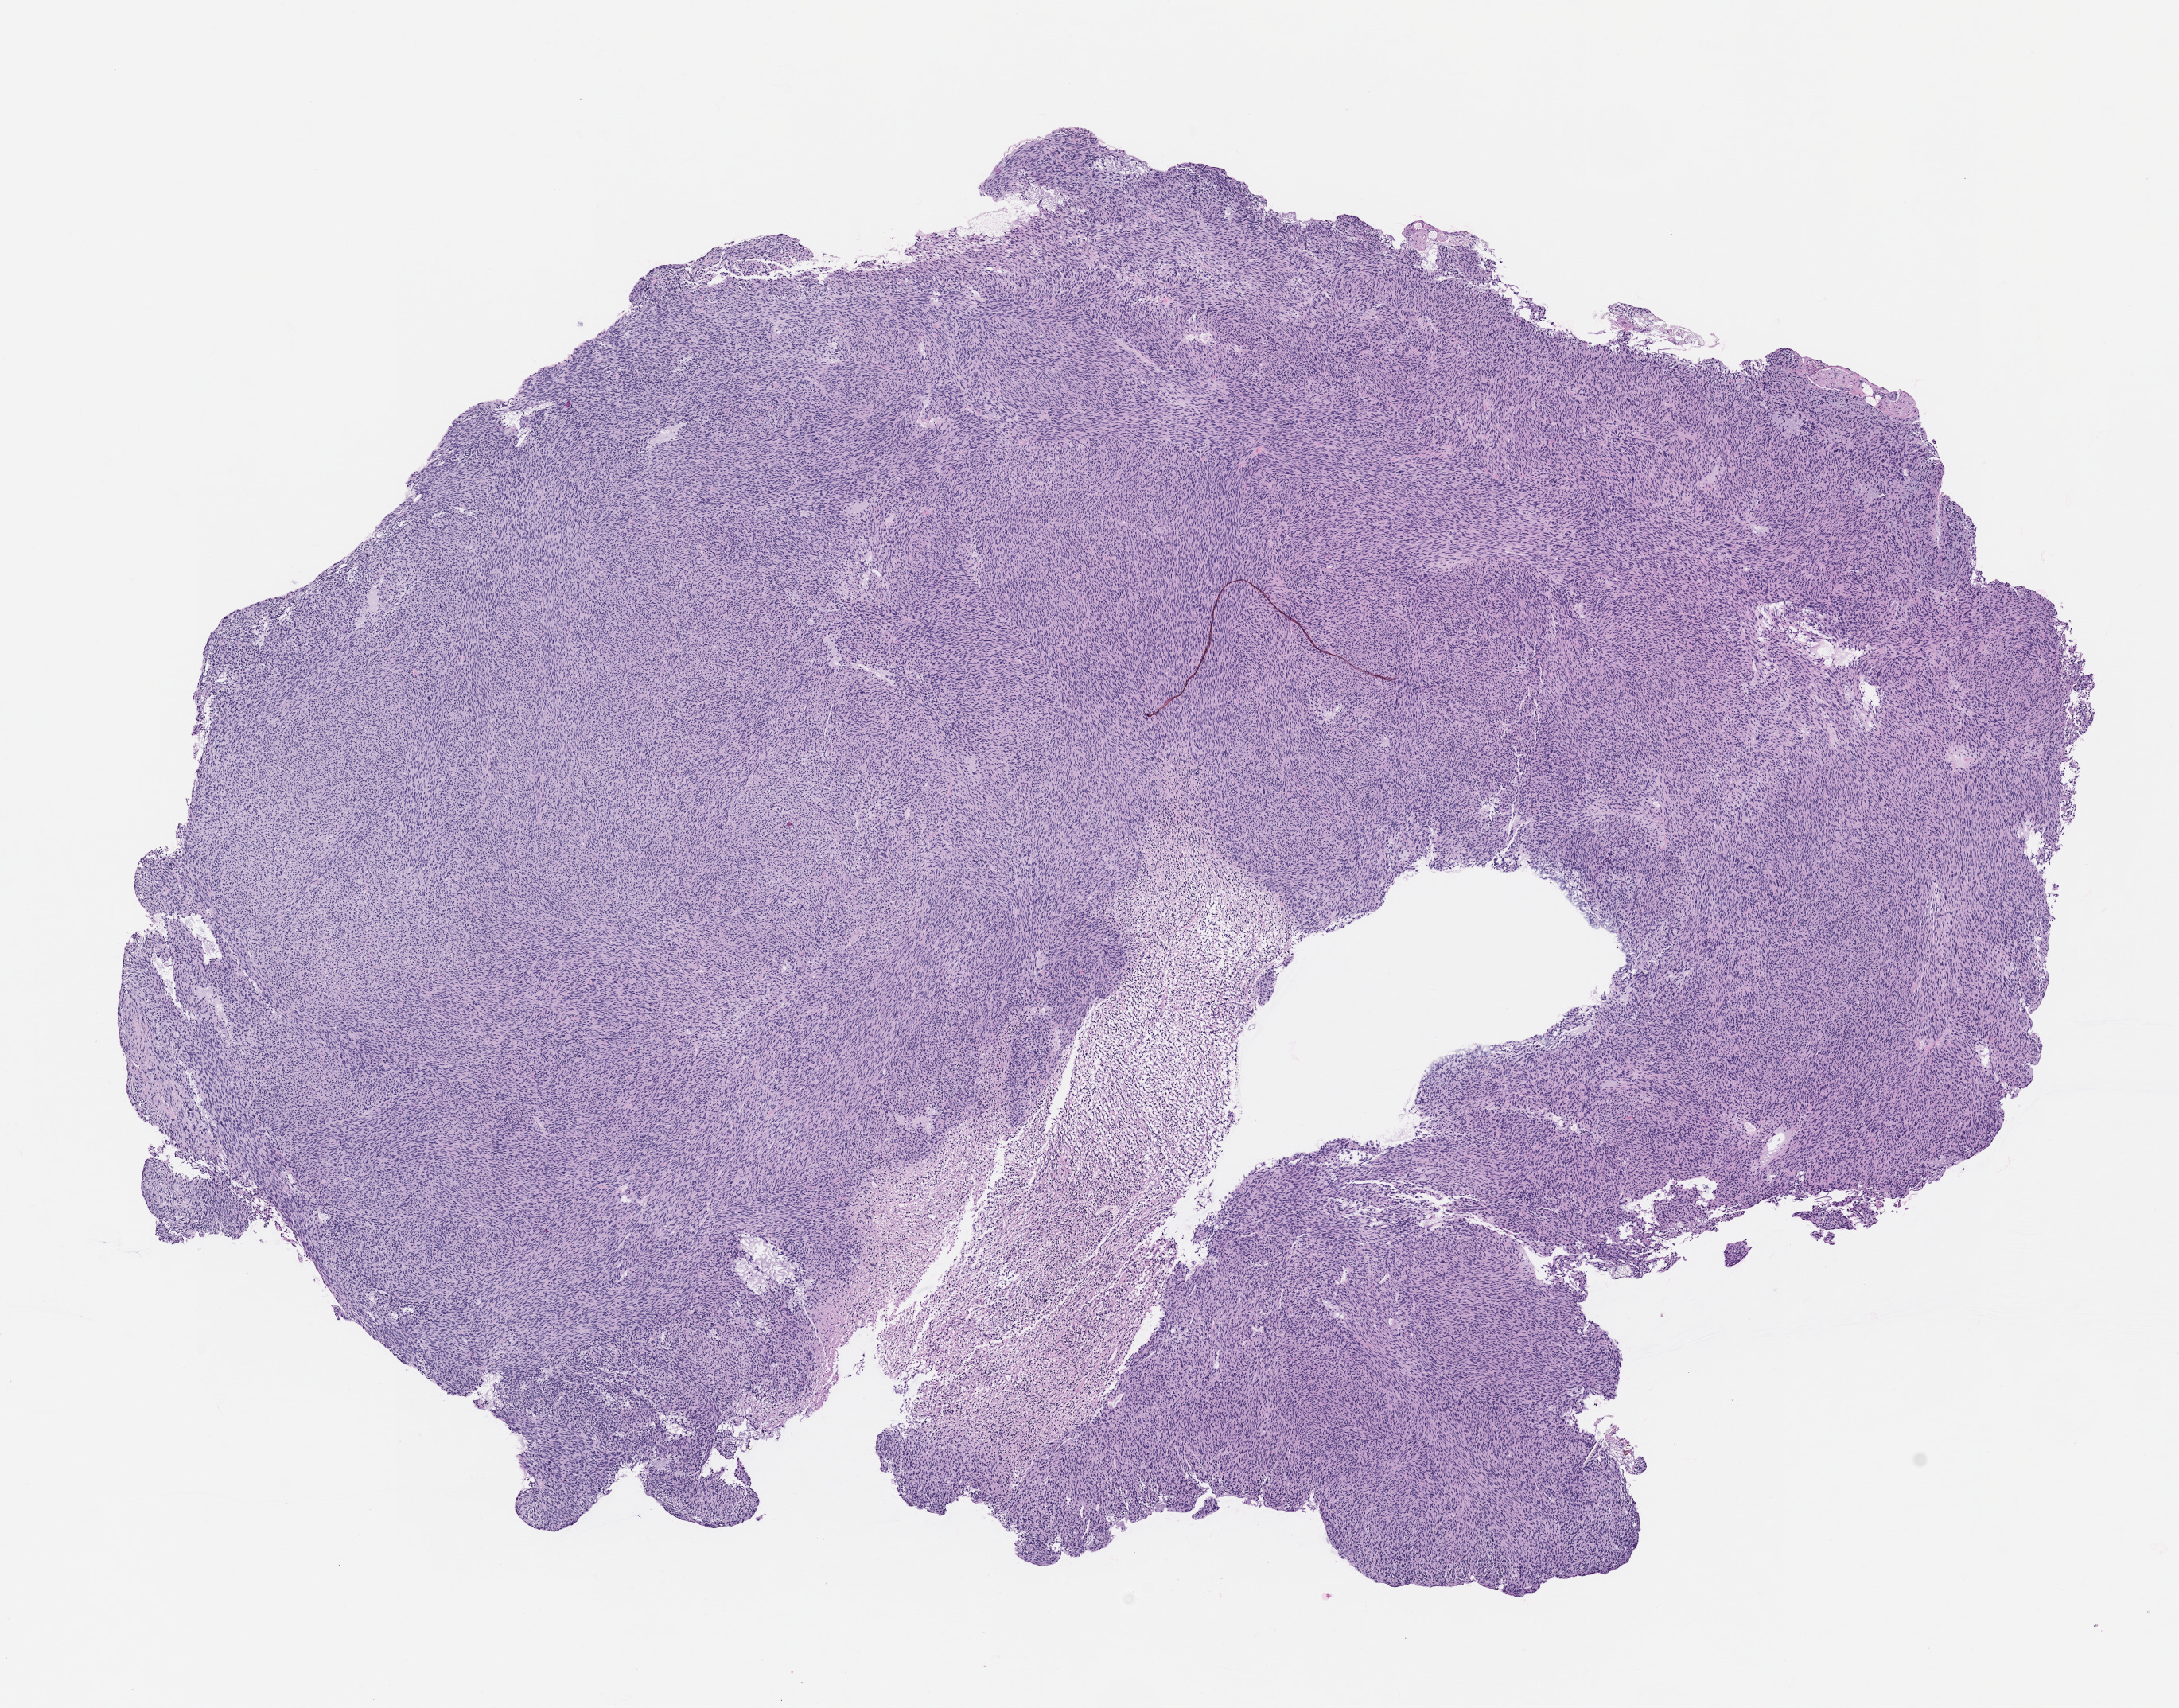
Whole-slide image, hematoxylin and eosin (H&E): patient-derived xenograft (human tumor grown in a mouse), passage 2 — shown as a low-resolution overview of the whole scanned area (about 11.0 x 8.6 mm). FFPE section. Originating tumor site category: uterus.
Originating patient diagnosis: Leiomyosarcoma.